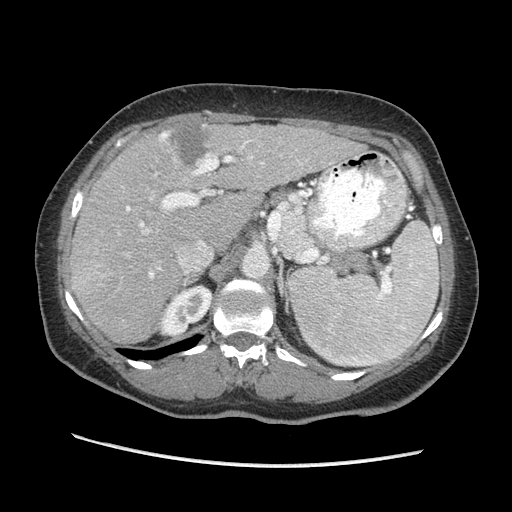
Contrast-enhanced abdominal CT (liver protocol), one axial slice; position 134 of 170 along the scan axis; 140 kVp; soft-tissue window (W 400 / L 40 HU); 2.5 mm slice thickness; 512 × 512 image matrix. Case-level facts recorded for this patient, not image findings: diagnosis: hepatocellular carcinoma (patient treated with transarterial chemoembolisation; whether this scan precedes or follows treatment is not stated here); TNM stage (as recorded): Stage-II; Child-Pugh class: A; tumour differentiation: no biopsy; tumour nodularity: multinodular.
Structures marked on this image (semi-automatically segmented with operator editing):
- liver parenchyma outside the tumour (the mass and vessels are separate outlines, so this box may not span the whole liver): box from (x=70, y=124) to (x=366, y=344) px
- mass: (x=158, y=119)–(x=207, y=164)
- liver vessels: (x=97, y=141)–(x=302, y=278)